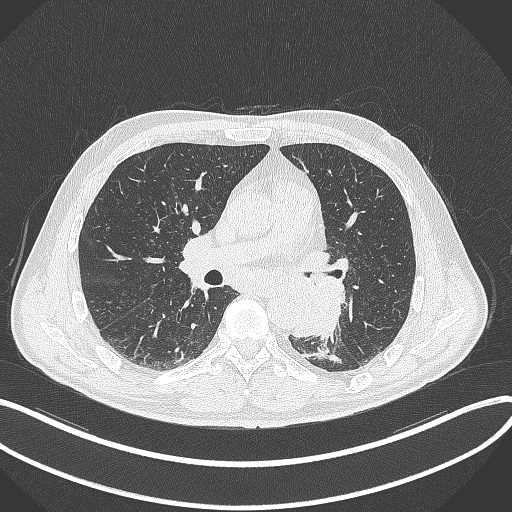
Chest CT, one axial slice; position 182 of 329 along the scan axis; reconstruction kernel B70f; 120 kVp; lung window (W 1500 / L -600 HU); 512 × 512 image matrix, field of view 400 × 400 mm. Male patient, age 59 years. From the clinical record (not read from this slice): clinical TNM (as recorded): T2a N2 M0.
Outlined on this slice (rectangle marked by the reading radiologist):
- lung tumour (recorded histology: squamous cell carcinoma): bounding box [x1, y1, x2, y2] px = [287, 276, 347, 344]